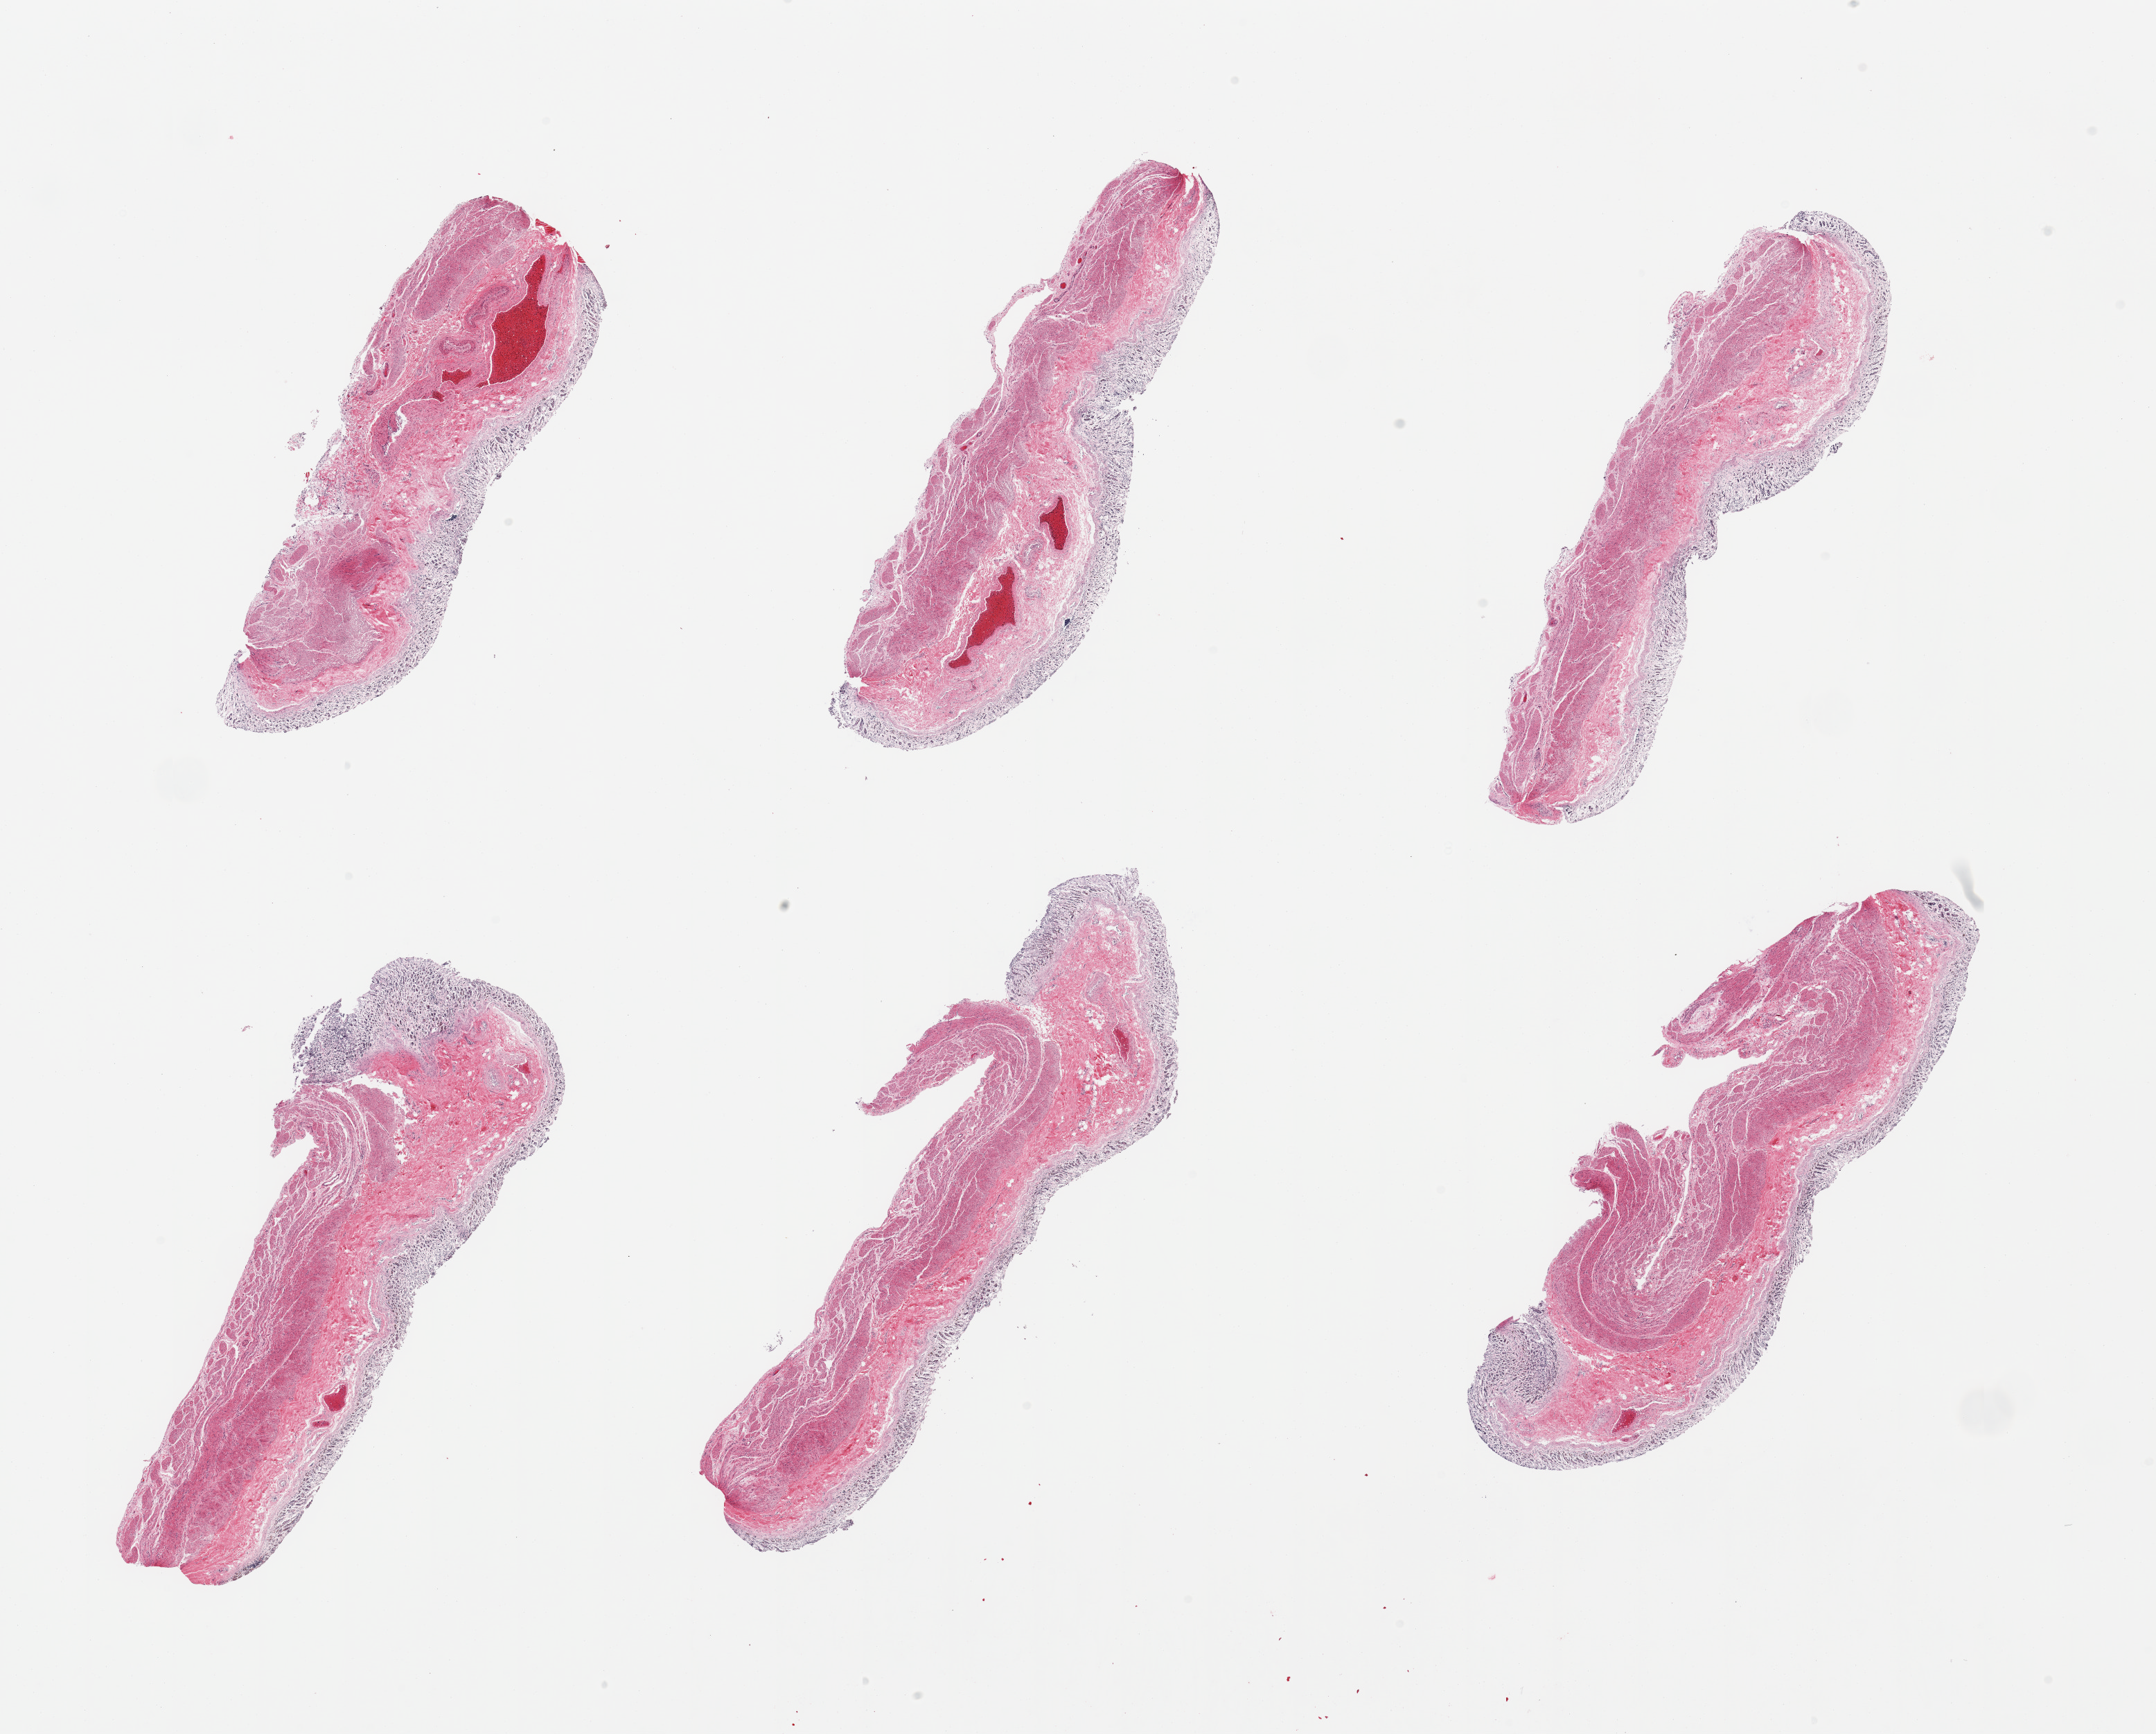
Digitized H&E-stained section — whole scanned area (about 24.6 x 19.8 mm) shown as a low-resolution overview. PAXgene-fixed paraffin-embedded (PFPE) section. Section of stomach (target tissue). Tissue donor sample. Male donor.
Review note (as recorded): 6 pieces, target mucosa up to ~0.4mm layer, totally autolyzed/sloughing.